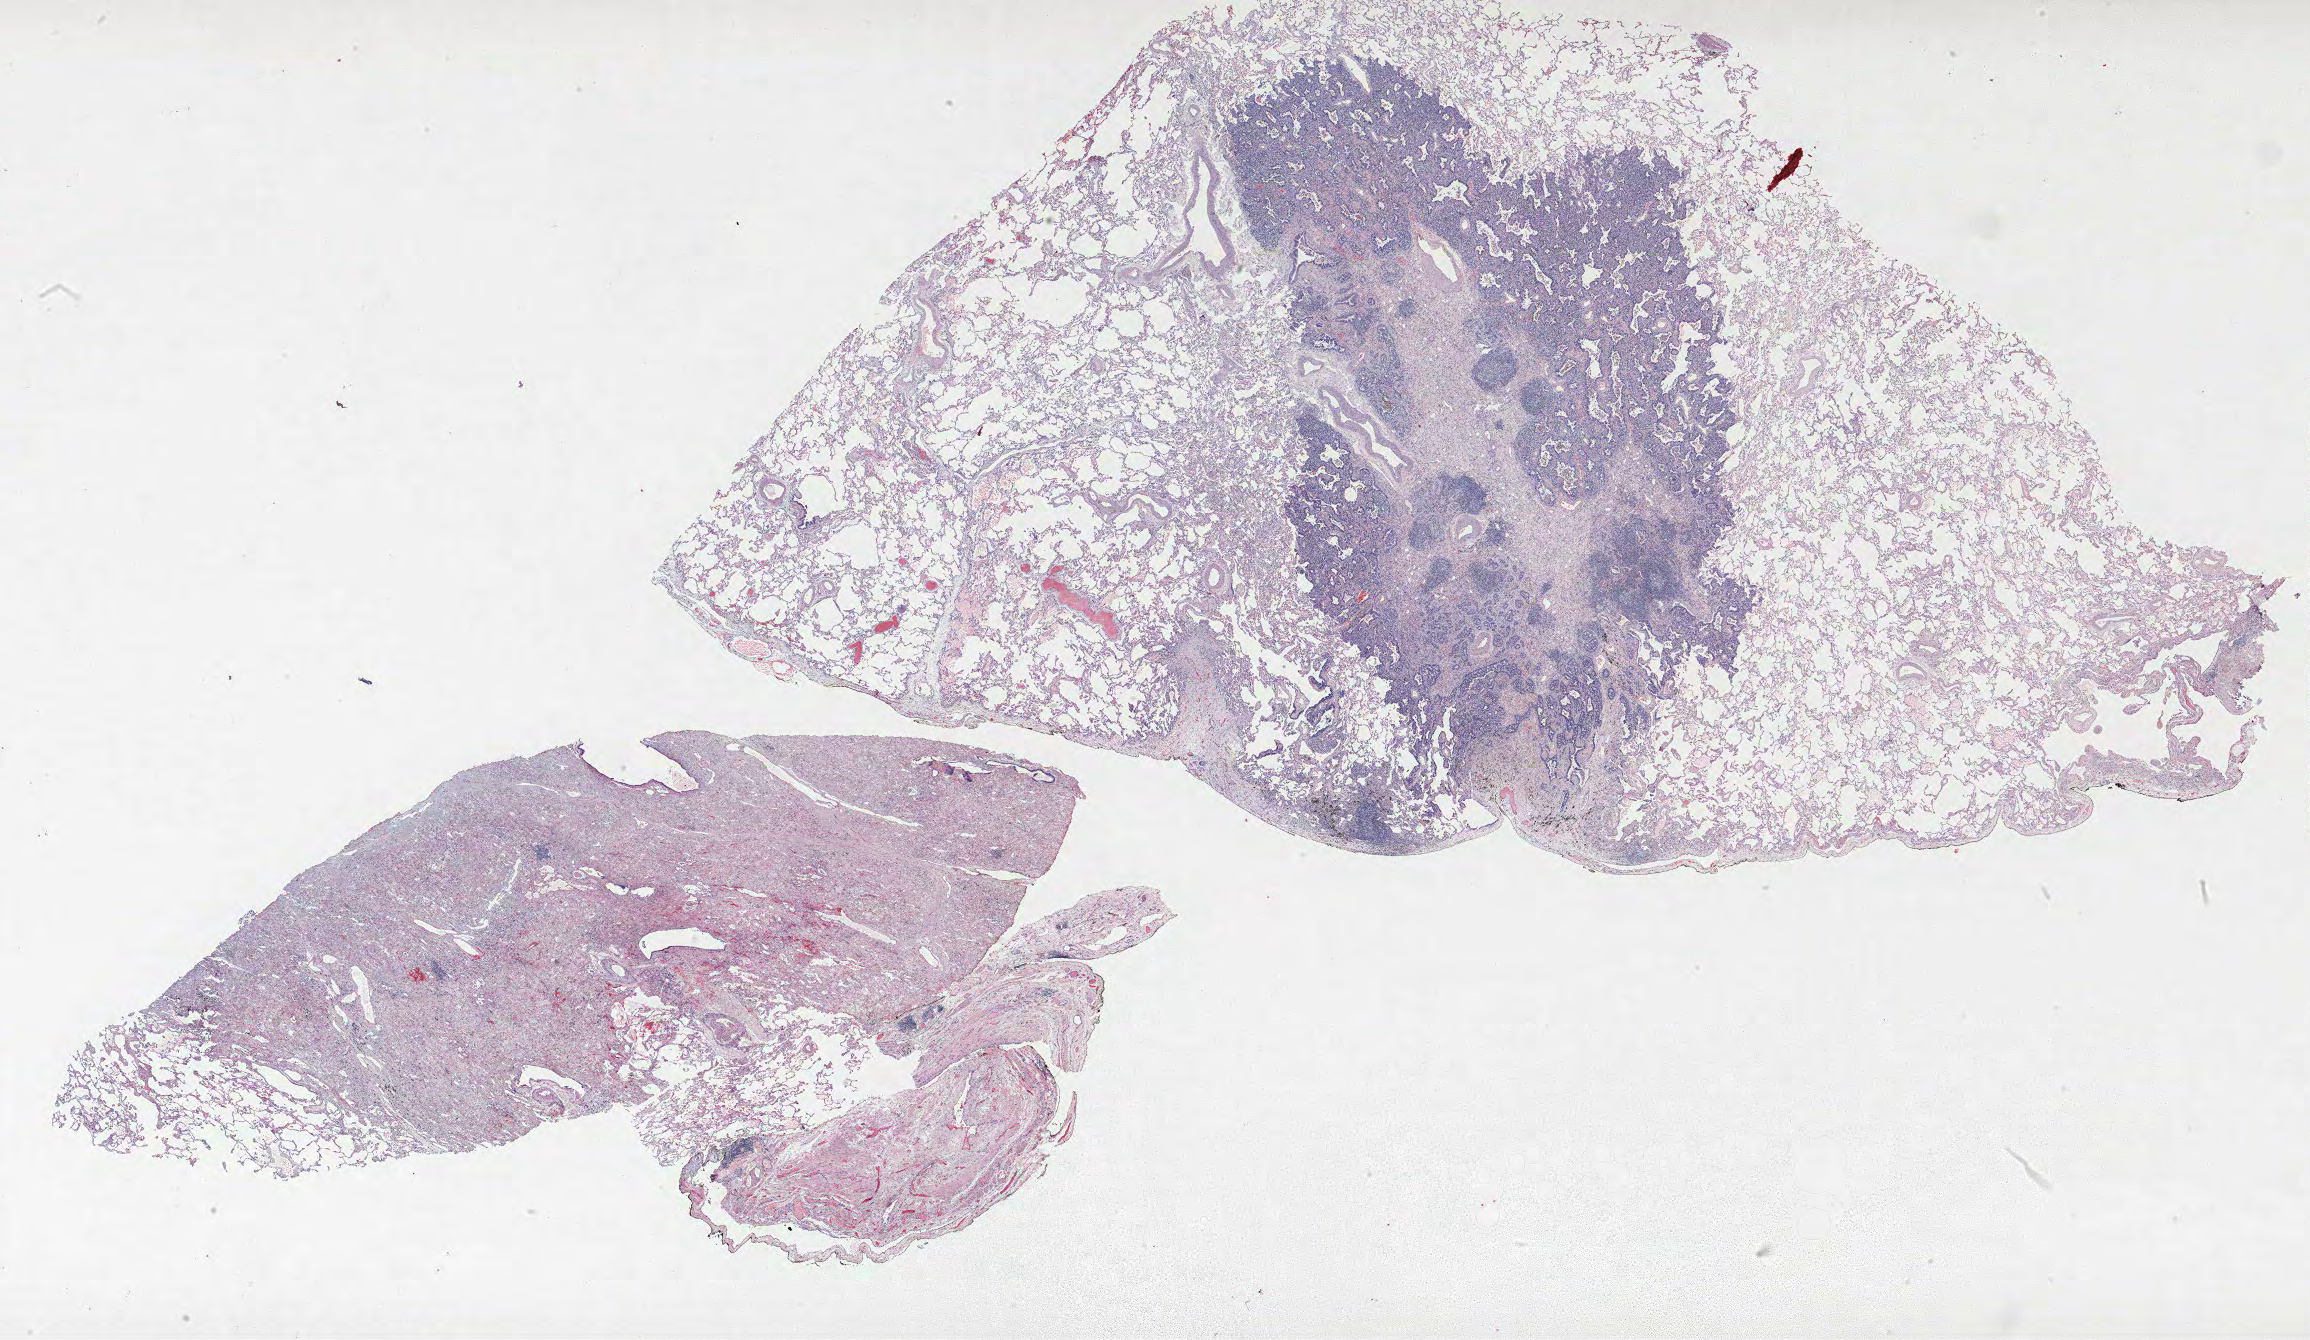
Whole-slide histology image, H&E — whole scanned area (about 37.0 x 21.4 mm, from a 40x scan) shown as a low-resolution overview. FFPE section. Lung tissue. Female patient, aged 67 at enrolment. Current smoker at enrolment. Grade: moderately differentiated (G2).
- stage (AJCC 6th edition): IA
- participant's lung-cancer diagnosis: Adenocarcinoma, NOS (ICD-O-3 8140/3)
- ICD-O-3 topography: upper lobe of lung (C34.1)
- primary tumour location (clinical record): right upper lobe
- tumour size (pathology): 14 mm
- note: participant had 2 primary lung cancers recorded; fields above describe the first